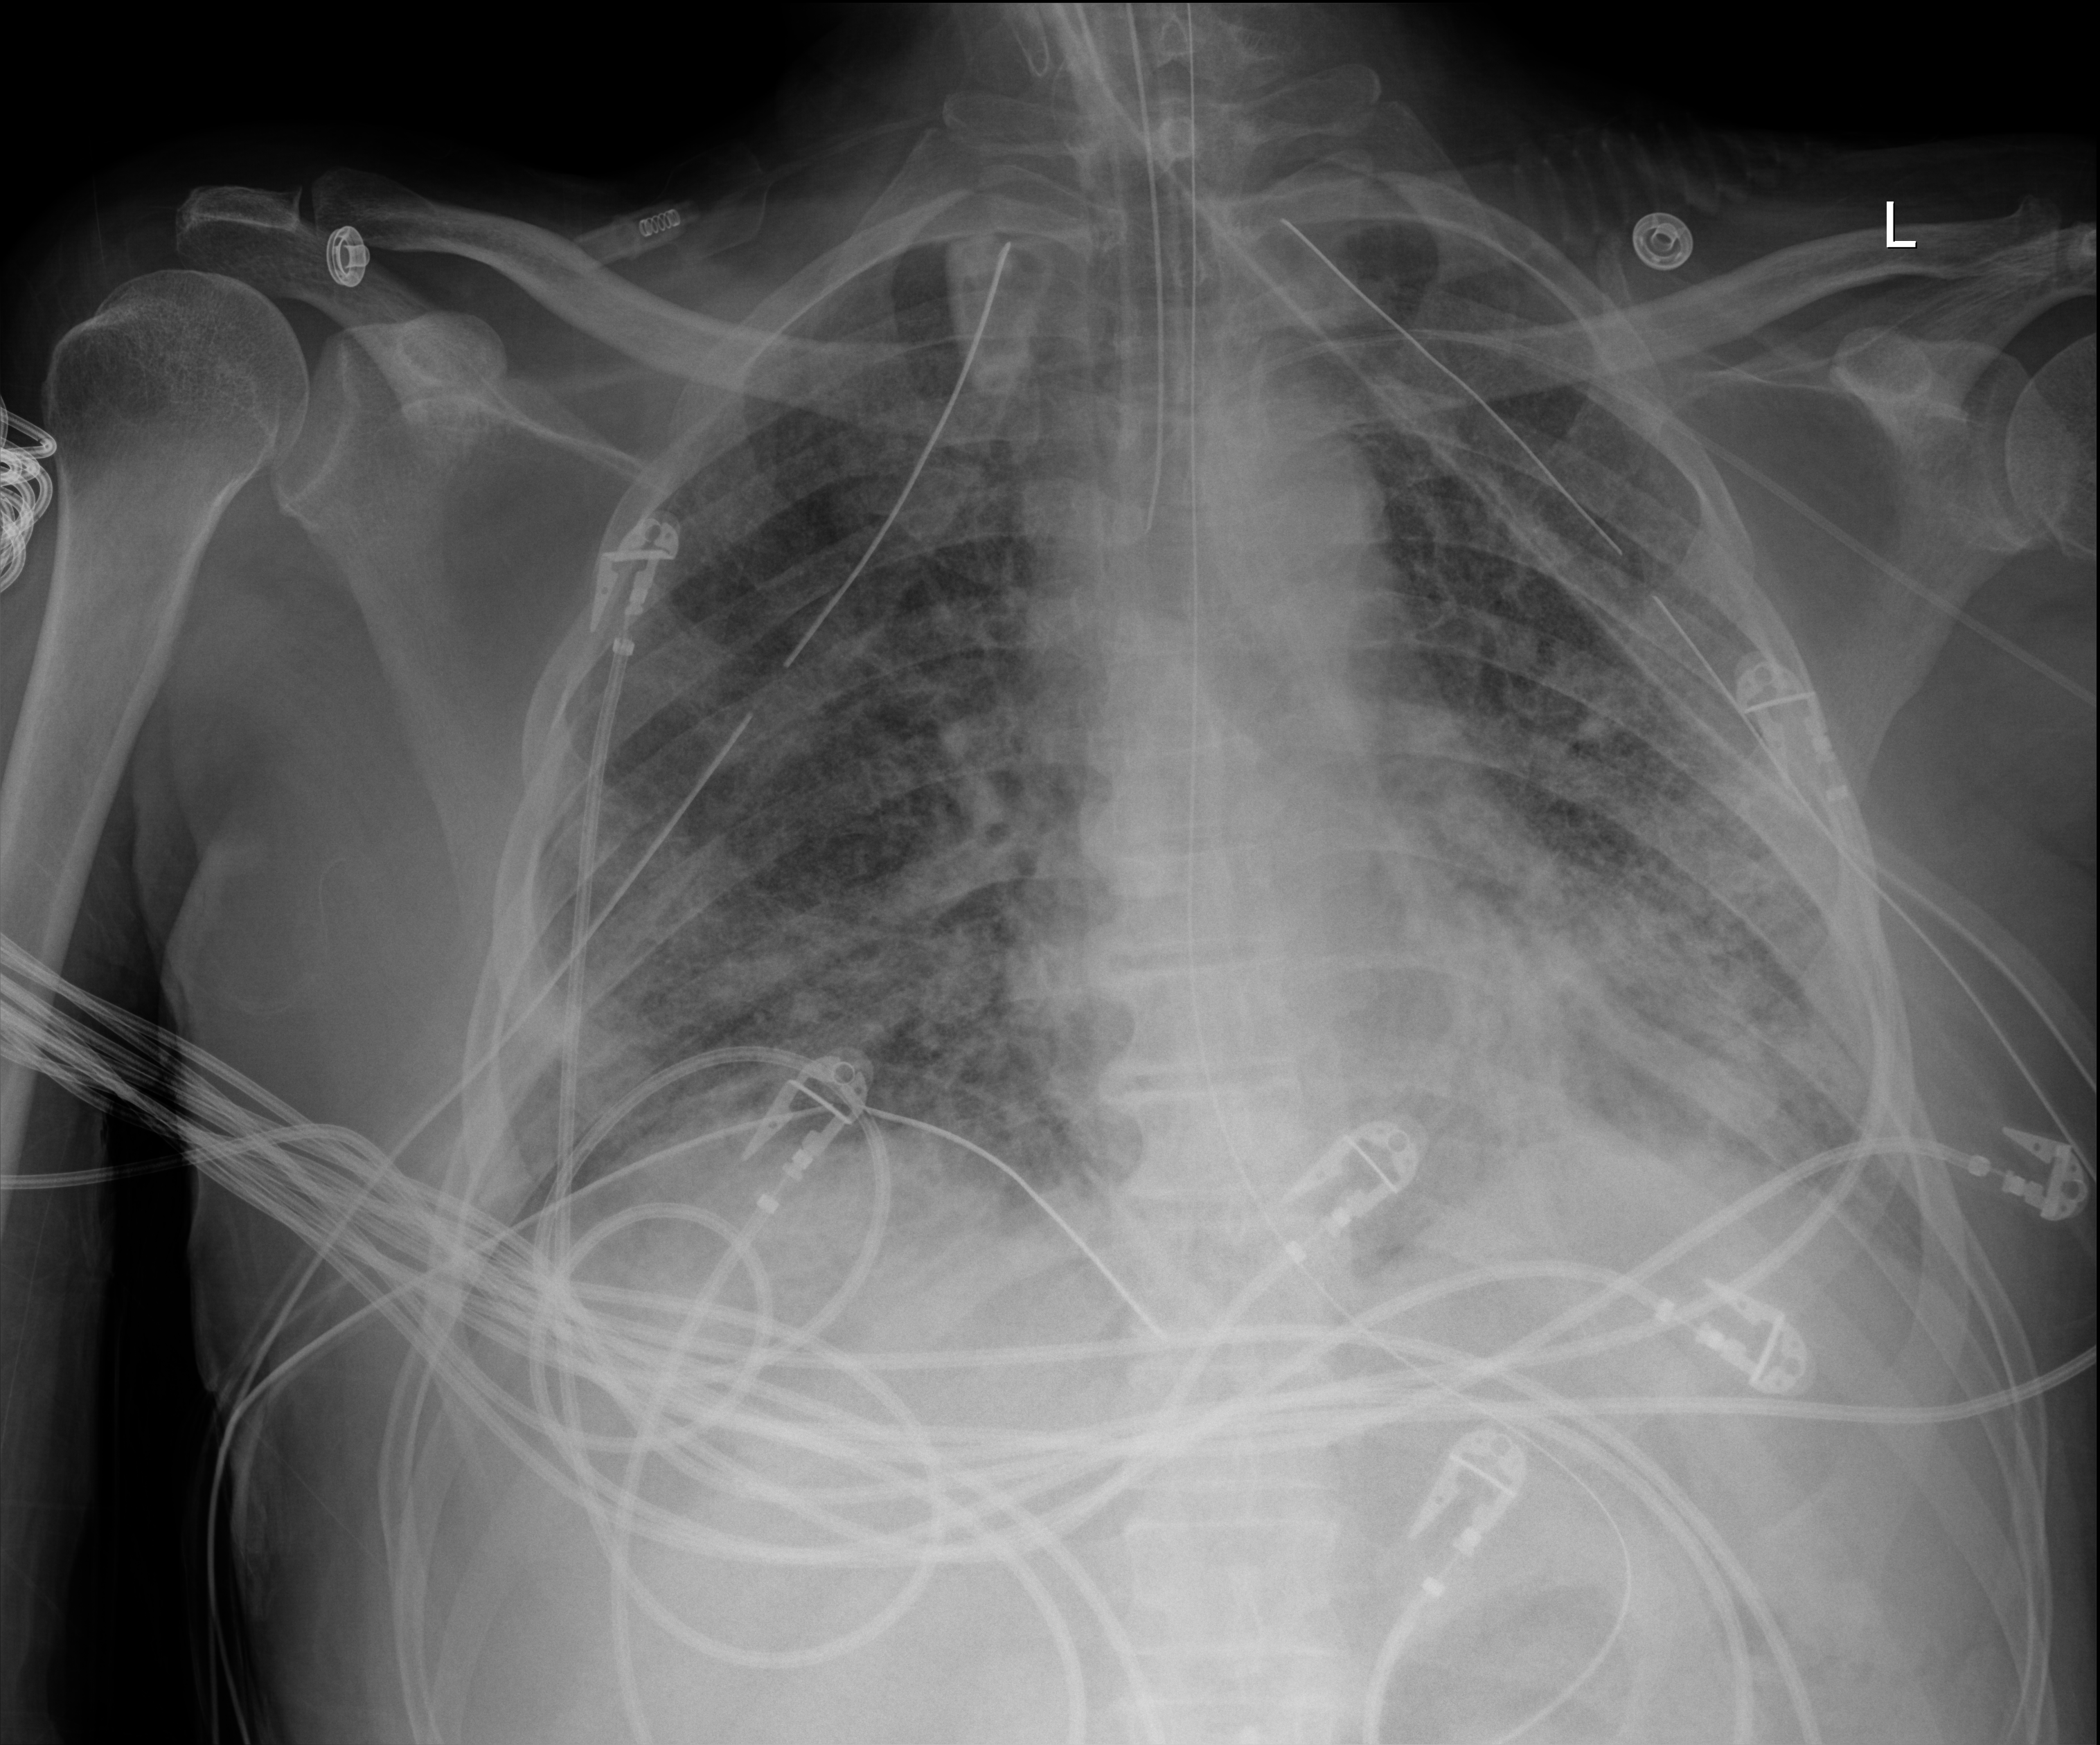
Bedside chest radiograph (digital radiography); anteroposterior (AP) projection. Male patient hospitalised with COVID-19, age 18–59 years.
From the hospital-stay record, not from the radiograph (when in the stay this image was taken is not recorded):
- admitted to intensive care during this hospital stay: yes
- mechanically ventilated during this hospital stay: yes